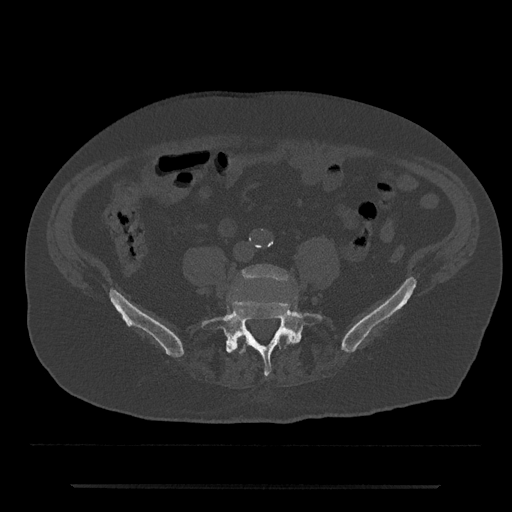
CT including the spine, one axial slice. Position 304 of 797 along the scan axis. Bone window (W 1800 / L 400 HU). 512 × 512 image matrix, field of view 434 × 434 mm. Male patient, age 80 years. Case-level facts recorded for this patient, not image findings: primary cancer: prostate; vertebrae with lytic lesions (as recorded): L1, T11.
Structures marked on this image (semi-automatically segmented with operator editing):
- L4 vertebra: bounding box (x1, y1, x2, y2) in pixels: (241, 265, 289, 339)
- L5 vertebra: (201, 299, 323, 376)